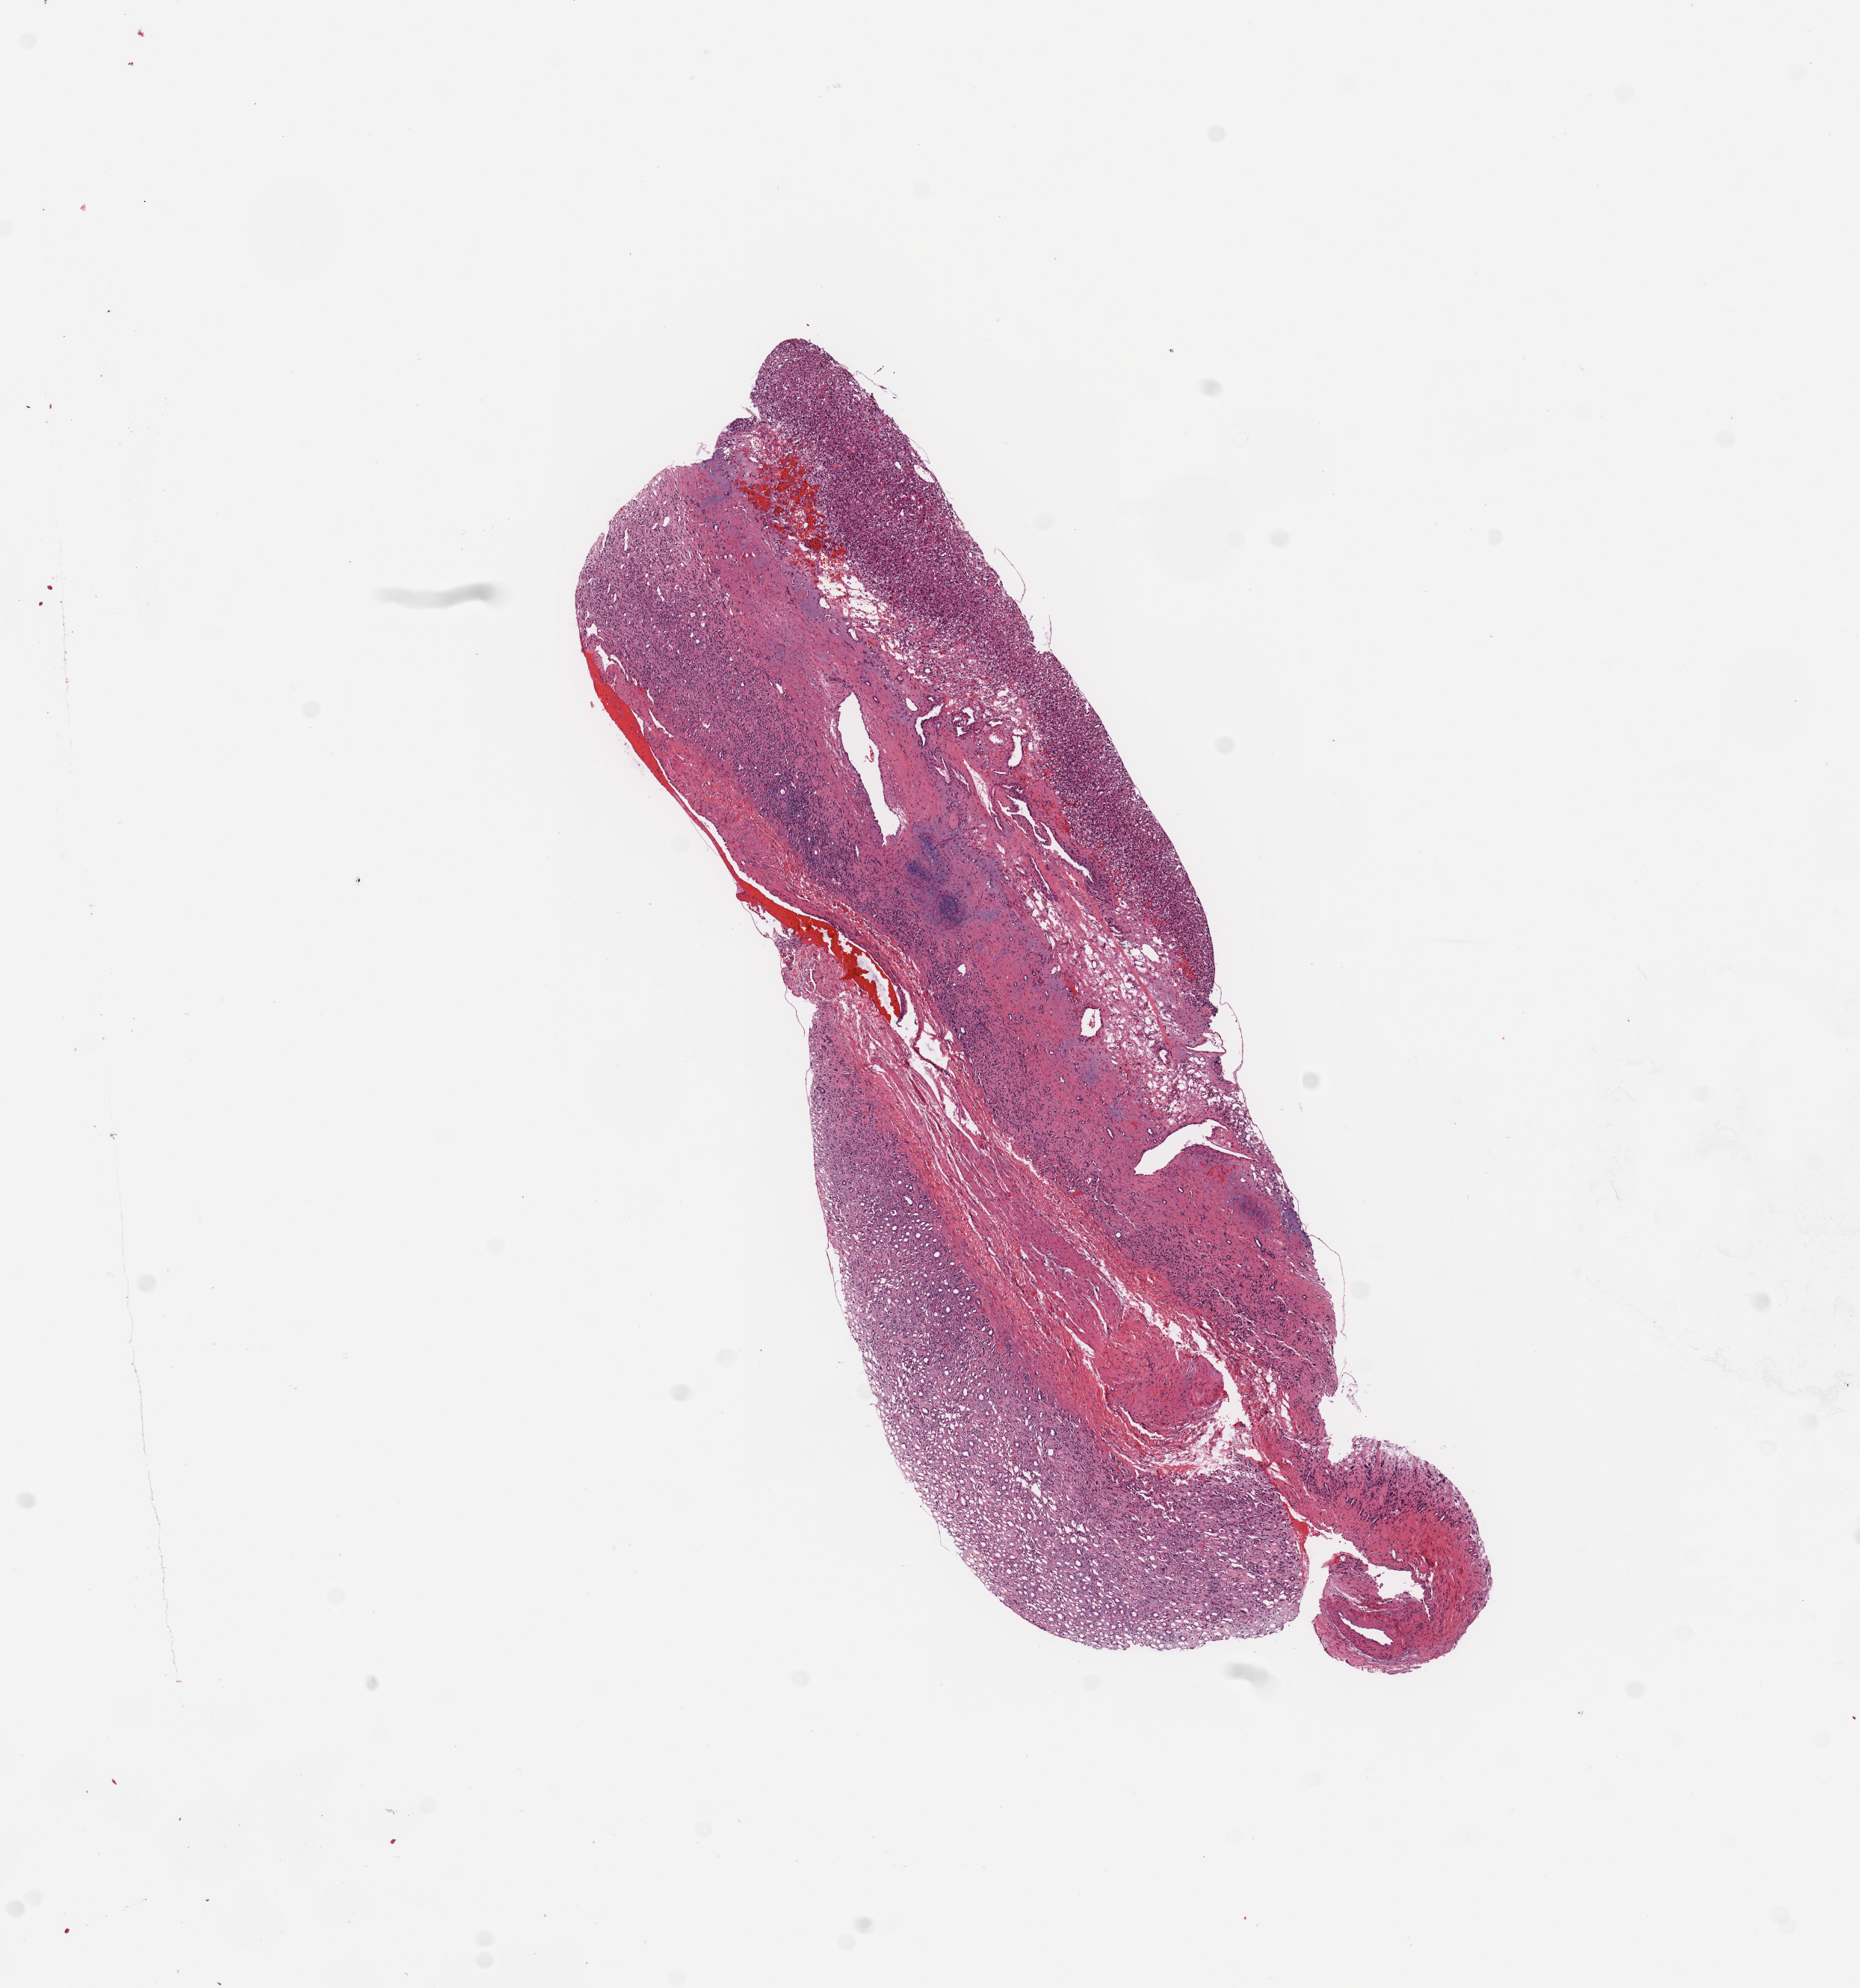
Digitized H&E tissue section (whole slide) — shown as a low-resolution overview of the whole scanned area (about 9.8 x 10.5 mm), kidney, tumour tissue. Patient: female, age 57 years. Histologic grade: G2 (moderately differentiated).
Primary tumour site (as recorded): lower pole. AJCC pathologic stage: I. Histologic diagnosis: Renal cell carcinoma, NOS.